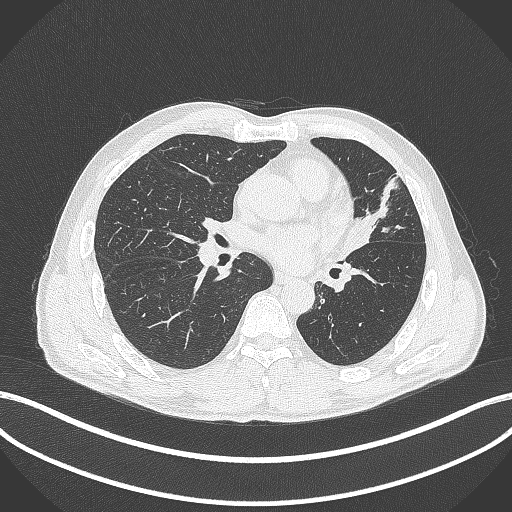
Chest CT, one axial slice. Position 215 of 429 along the scan axis. Reconstruction kernel B70f. 120 kVp. Lung window (W 1500 / L -600 HU). 1 mm slice thickness. 512 × 512 image matrix, field of view 400 × 400 mm. Male patient, age 57 years. Case-level facts recorded for this patient, not image findings: clinical TNM (as recorded): T2b N0 M0.
Outlined on this slice (rectangle marked by the reading radiologist):
- lung tumour (recorded histology: squamous cell carcinoma): box from (x=340, y=205) to (x=373, y=261) px